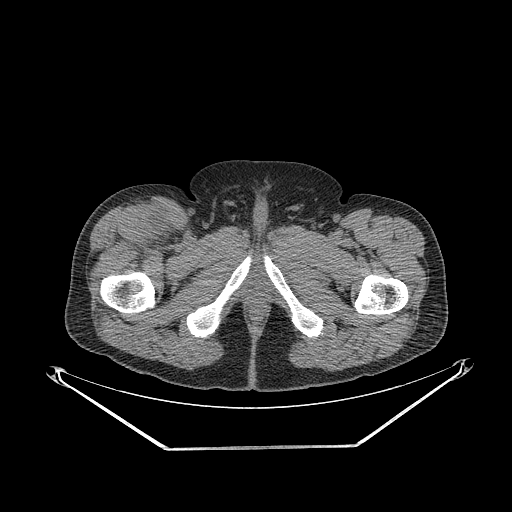
CT of an extremity soft-tissue mass (from a PET/CT study), one axial slice; position 306 of 311 along the scan axis; 140 kVp; soft-tissue window (W 400 / L 40 HU); 512 × 512 image matrix, field of view 500 × 500 mm. Male patient. From the clinical record (not read from this slice): histological type: pleiomorphic leiomyosarcoma; grade: intermediate; site of the primary tumour: right thigh.
Structures marked on this image (expert contour drawn on MRI and transferred to this co-registered scan by the dataset authors):
- gross tumour volume including surrounding oedema: bounding box [x1, y1, x2, y2] px = [139, 206, 175, 245]
- gross tumour volume (mass): [155, 217, 174, 241]